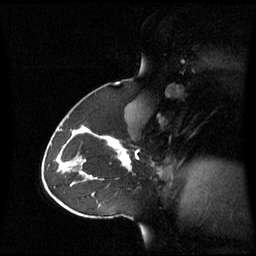
Breast MRI (dynamic contrast-enhanced), one sagittal slice; slice 40 of 60 in the series (ordered by position); dynamic contrast-enhanced series, image 2 of 3 at this slice position (ordered by acquisition); 1.5 T; TE 4.2 ms, TR 8.4 ms; 2.8 mm slice thickness; 256 × 256 image matrix. Patient: female, 43 years. Case-level facts recorded for this patient, not image findings: setting: breast cancer imaged before/during neoadjuvant chemotherapy; receptor status: triple-negative.
Annotated regions visible in this slice (semi-automatically segmented with operator editing):
- analysis volume of interest (the breast-tissue region the enhancement analysis was run in; not a lesion): bounding box [x1, y1, x2, y2] px = [62, 124, 137, 180]
- tumour enhancement mask (voxels above the 70 % enhancement threshold inside the analysis volume of interest): [93, 134, 130, 167]